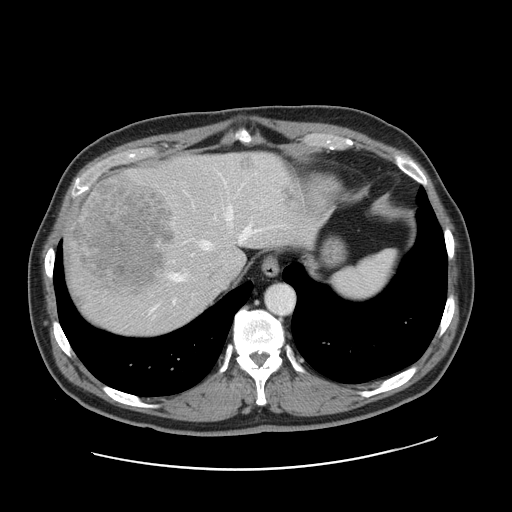
Contrast-enhanced abdominal CT, one axial slice; position 132 of 178 along the scan axis; 120 kVp; intravenous contrast given; soft-tissue window (W 400 / L 40 HU); 512 × 512 image matrix, field of view 403 × 403 mm. Male patient, age 63 years. Case-level facts recorded for this patient, not image findings: diagnosis: colorectal cancer liver metastases, imaged before liver resection; multiple liver metastases: yes; largest metastasis: 8 cm.
Outlined on this slice (outlined manually by an expert reader):
- hepatic veins: bounding box (x1, y1, x2, y2) in pixels: (172, 209, 250, 281)
- liver: (64, 152, 305, 335)
- planned liver remnant (the part of the liver to remain after resection): (159, 154, 305, 280)
- liver metastasis: (242, 157, 253, 169)
- liver metastasis: (67, 177, 175, 296)